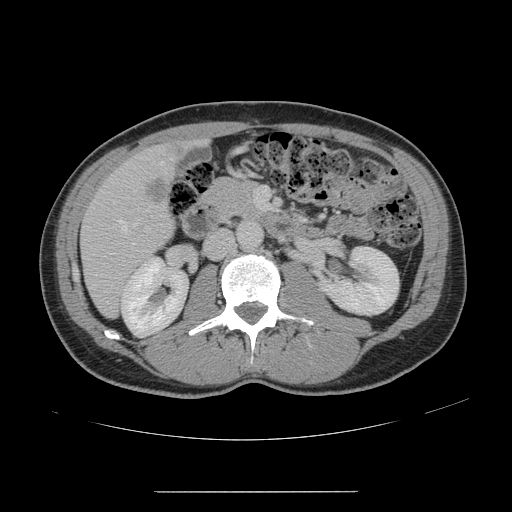
Contrast-enhanced abdominal CT, one axial slice; slice 59 of 178 in the series (ordered by position); intravenous contrast given; soft-tissue window (W 400 / L 40 HU); 2.5 mm slice thickness; 512 × 512 image matrix, field of view 401 × 401 mm. Male patient, age 53 years. Case-level facts recorded for this patient, not image findings: diagnosis: colorectal cancer liver metastases, imaged before liver resection; multiple liver metastases: yes; largest metastasis: 2.4 cm; disease in both lobes: no.
Outlined on this slice (manually delineated by an expert):
- hepatic veins: bounding box [x1, y1, x2, y2] px = [102, 161, 163, 245]
- liver: [82, 141, 195, 315]
- portal vein (with intrahepatic branches): [254, 187, 267, 210]
- liver metastasis: [173, 144, 185, 154]
- liver metastasis: [145, 179, 168, 204]